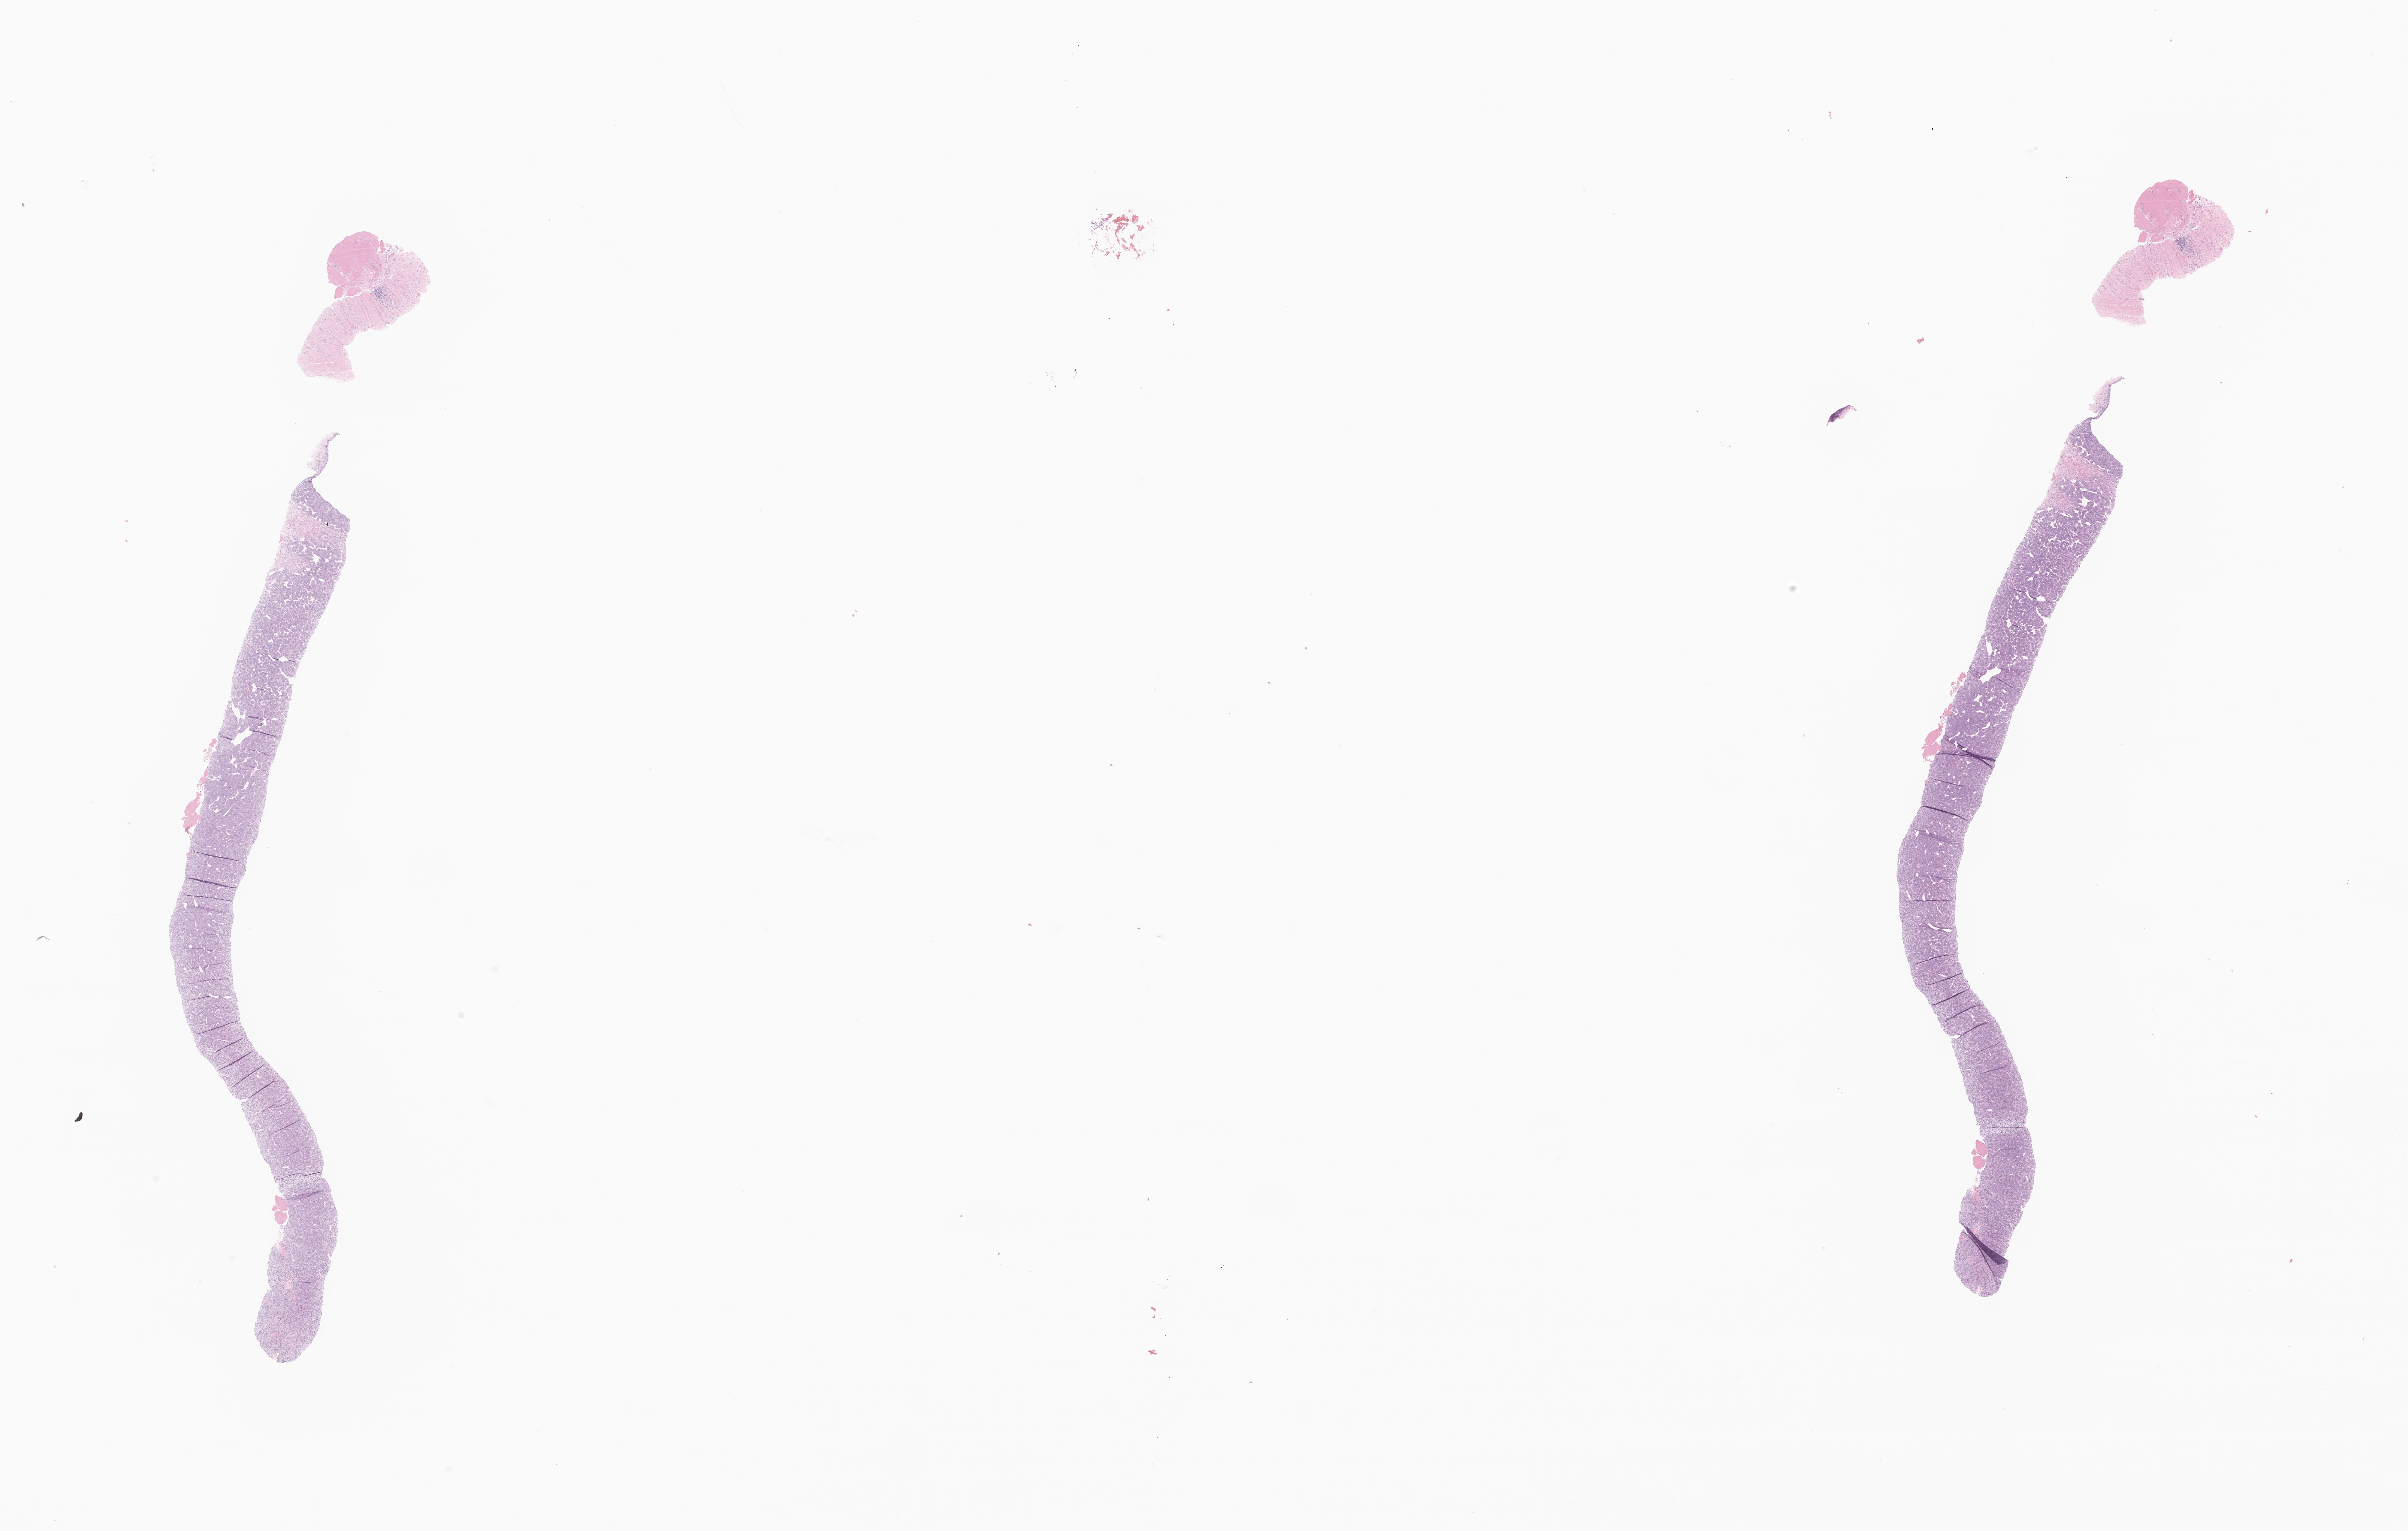
Whole-slide image, hematoxylin and eosin (H&E) stain of tumor tissue from the soft tissue of lower extremity, a low-resolution overview of the entire scanned area, about 27.1 x 17.2 mm. Formalin-fixed, paraffin-embedded (FFPE) tissue. Female patient, age 132 months.
Diagnosis: Undifferentiated sarcoma.